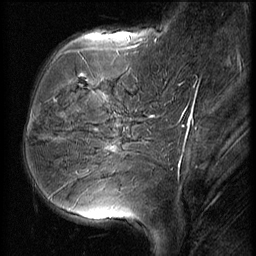
Breast MRI (dynamic contrast-enhanced), one sagittal slice. Position 17 of 56 along the scan axis. 3 images stored at this slice position (order not interpretable as contrast timing). 1.5 T. TE 4.2 ms, TR 9 ms. 2.5 mm slice thickness. 256 × 256 image matrix, field of view 180 × 180 mm. Patient: female, 51 years. Case-level facts recorded for this patient, not image findings: setting: breast cancer imaged before/during neoadjuvant chemotherapy; receptor status: HR-positive, HER2-negative.
Structures marked on this image (semi-automatically segmented with operator editing):
- analysis volume of interest (the breast-tissue region the enhancement analysis was run in; not a lesion): bounding box [x1, y1, x2, y2] px = [23, 56, 156, 165]
- tumour enhancement mask (voxels above the 140 % enhancement threshold inside the analysis volume of interest): [107, 148, 115, 151]